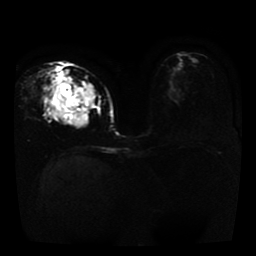
Breast MRI, one axial slice; position 17 of 41 along the scan axis; diffusion-weighted series; image 2 of 4 stored at this slice position (different b-values; order by instance number); 1.5 T; 5 mm slice thickness; 256 × 256 image matrix. Female patient.
Outlined on this slice (outlined manually by an expert reader):
- tumour on diffusion-weighted imaging: box from (x=52, y=68) to (x=95, y=124) px